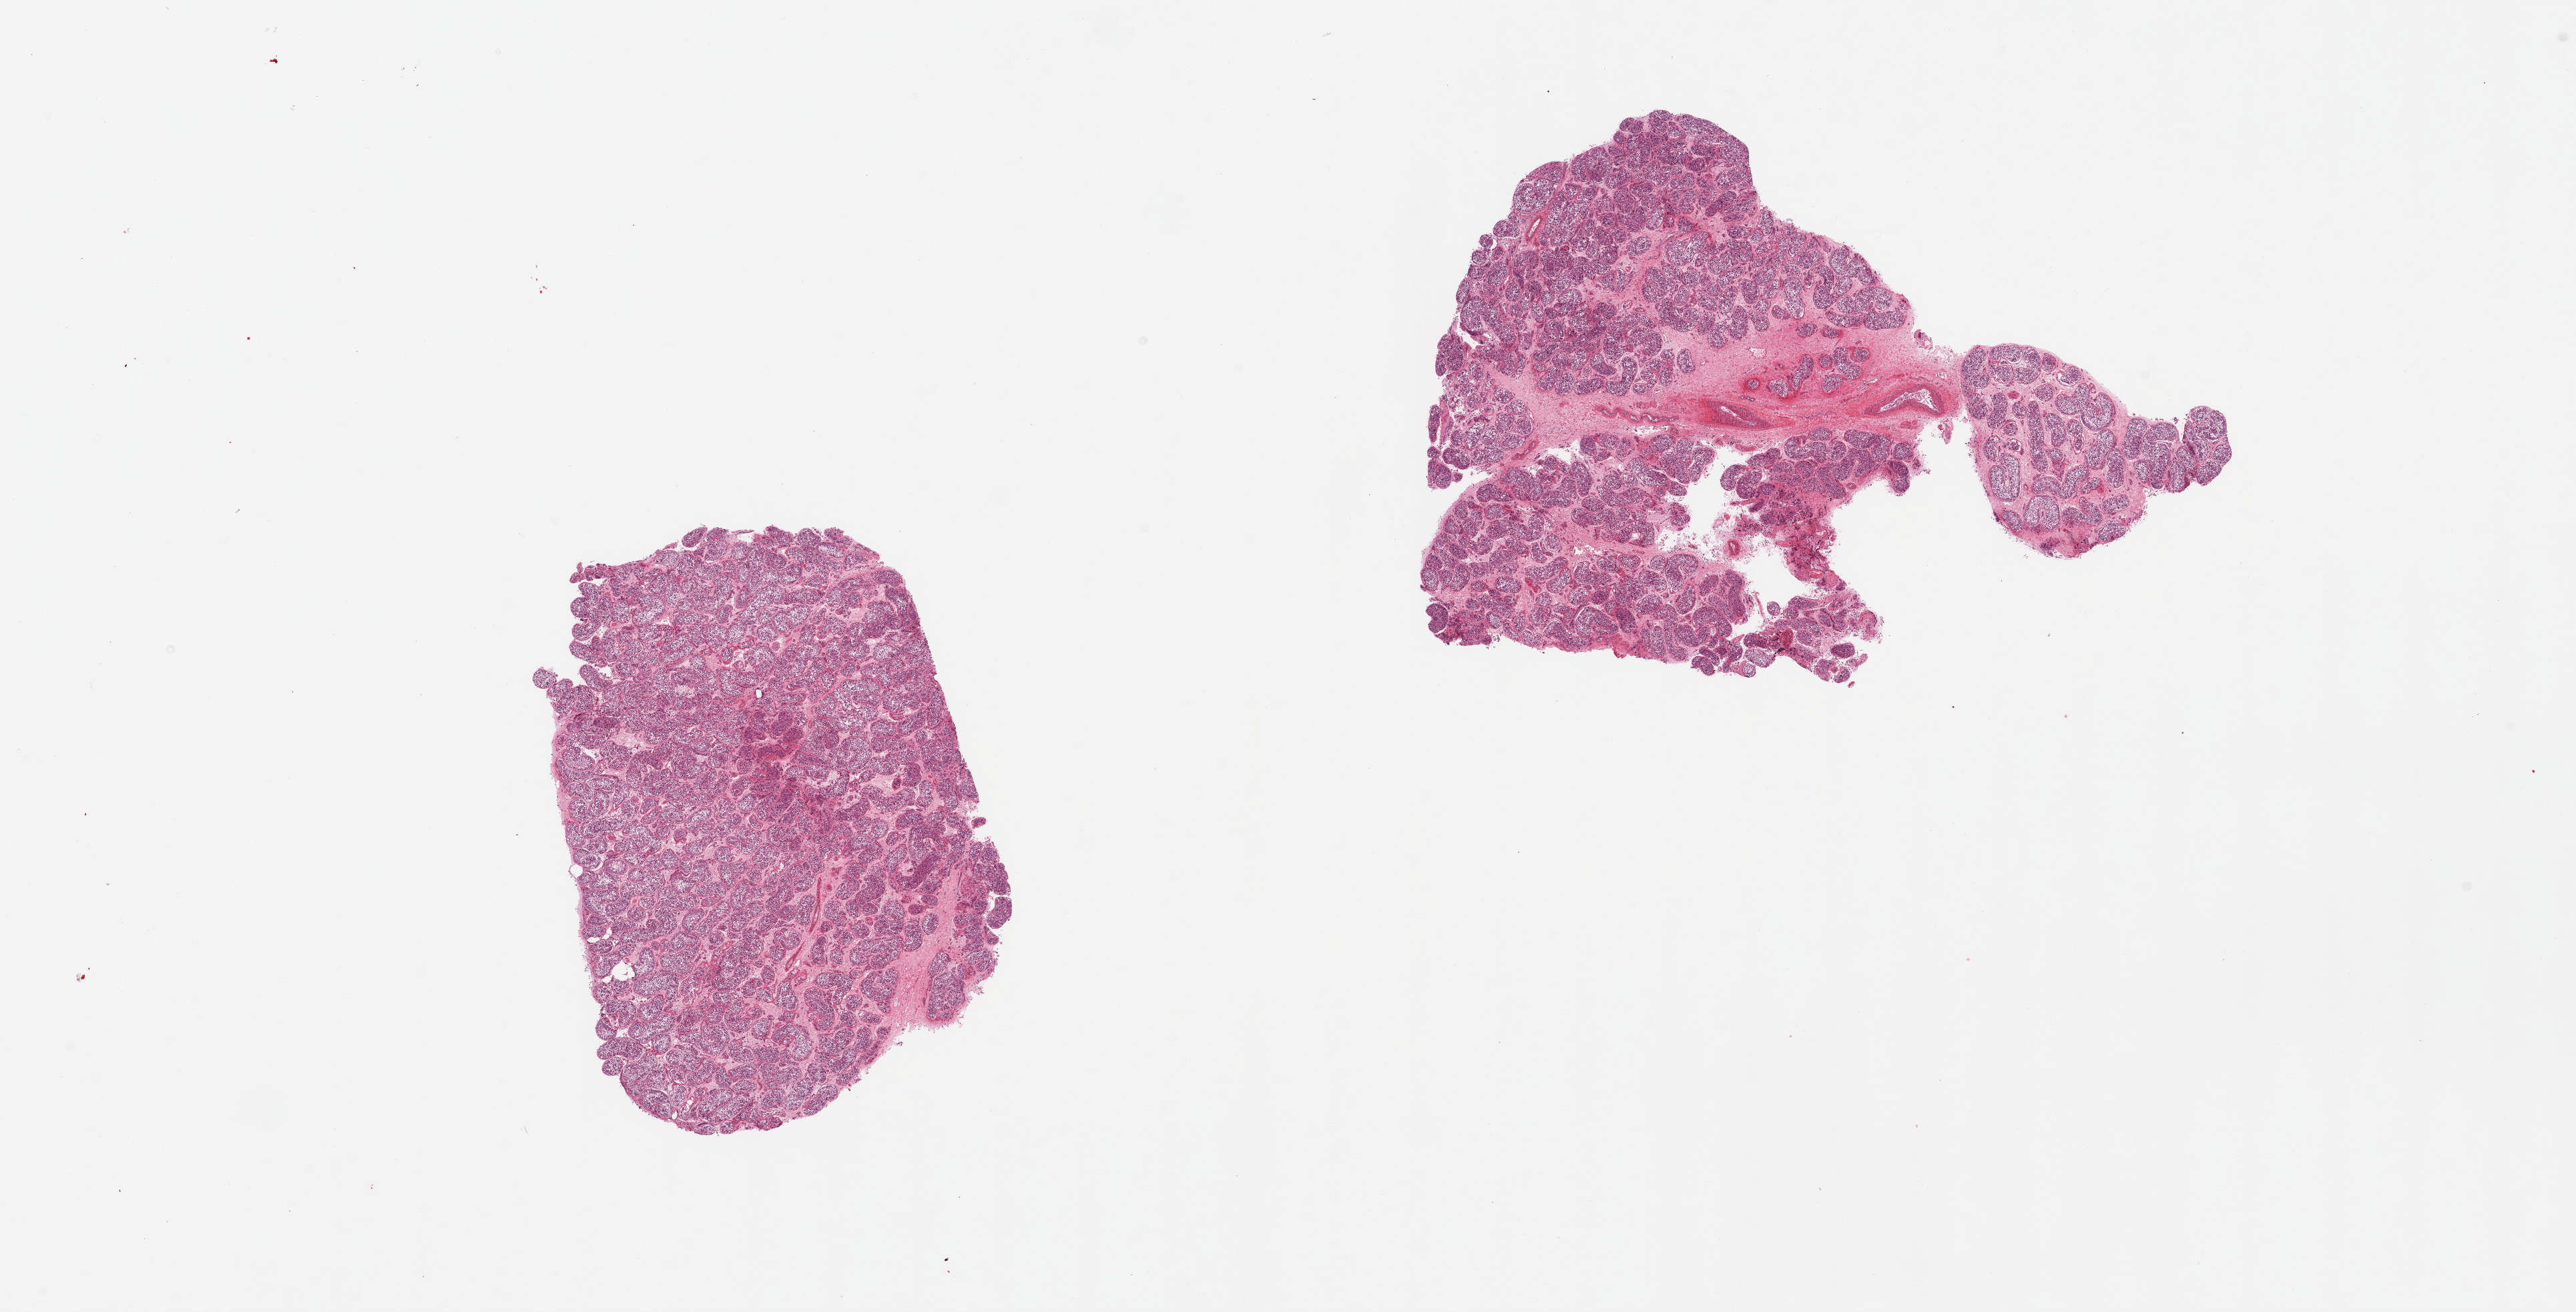
Hematoxylin and eosin (H&E) whole-slide image, shown as a low-resolution overview of the whole scanned area (about 30.5 x 15.5 mm, slide scanned at 20x). PAXgene-fixed paraffin-embedded (PFPE) section. Section of testis (target tissue). Donor tissue sample. Donor: male.
Pathologist's review note for this sample: 2 pieces; robust spermatogenesis.